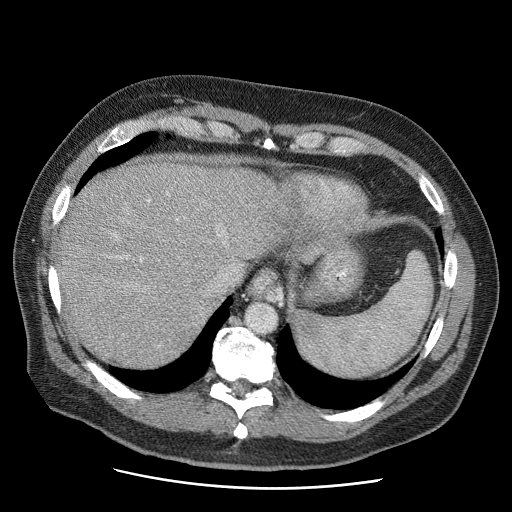
Contrast-enhanced abdominal CT (liver protocol), one axial slice. Position 48 of 81 along the scan axis. 120 kVp. Soft-tissue window (W 400 / L 40 HU). 512 × 512 image matrix, field of view 380 × 380 mm. Case-level facts recorded for this patient, not image findings: diagnosis: hepatocellular carcinoma (patient treated with transarterial chemoembolisation; whether this scan precedes or follows treatment is not stated here); TNM stage (as recorded): Stage-IIIA; Child-Pugh class: A; tumour differentiation: moderately differentiated; tumour nodularity: multinodular.
Outlined on this slice (semi-automatically segmented with operator editing):
- liver parenchyma outside the tumour (the mass and vessels are separate outlines, so this box may not span the whole liver): box from (x=57, y=160) to (x=366, y=366) px
- liver vessels: (x=148, y=200)–(x=220, y=236)